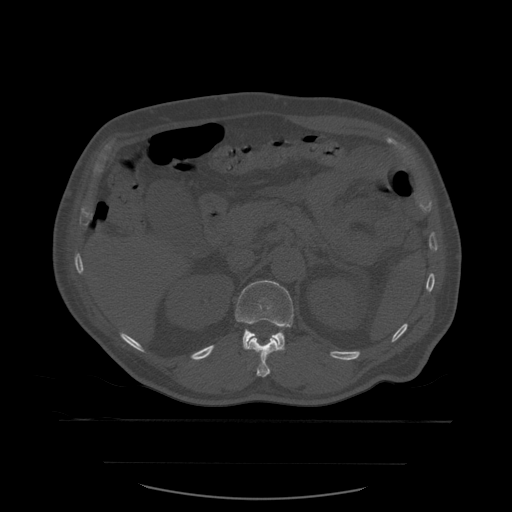
CT including the spine, one axial slice; slice 258 of 590 in the series (ordered by position); bone window (W 1800 / L 400 HU); 1.25 mm slice thickness; 512 × 512 image matrix, field of view 479 × 479 mm. Patient age 71 years. Case-level facts recorded for this patient, not image findings: primary cancer: lung.
Outlined on this slice (semi-automatic segmentation, software-assisted and operator-edited):
- L1 vertebra: bounding box [x1, y1, x2, y2] px = [235, 281, 294, 351]
- T12 vertebra: [243, 335, 282, 378]